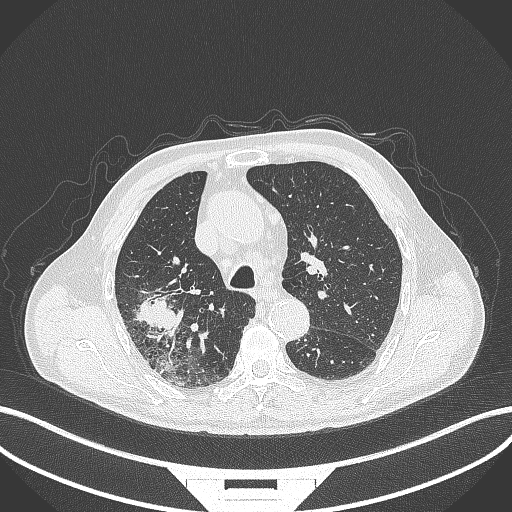
Chest CT, one axial slice; position 287 of 429 along the scan axis; 120 kVp; lung window (W 1500 / L -600 HU); 1 mm slice thickness; 512 × 512 image matrix, field of view 400 × 400 mm. Patient: male, 72 years. Case-level facts recorded for this patient, not image findings: clinical TNM (as recorded): T3 N2 M0.
Annotated regions visible in this slice (rectangle marked by the reading radiologist):
- lung tumour (recorded histology: adenocarcinoma): box from (x=134, y=288) to (x=188, y=338) px